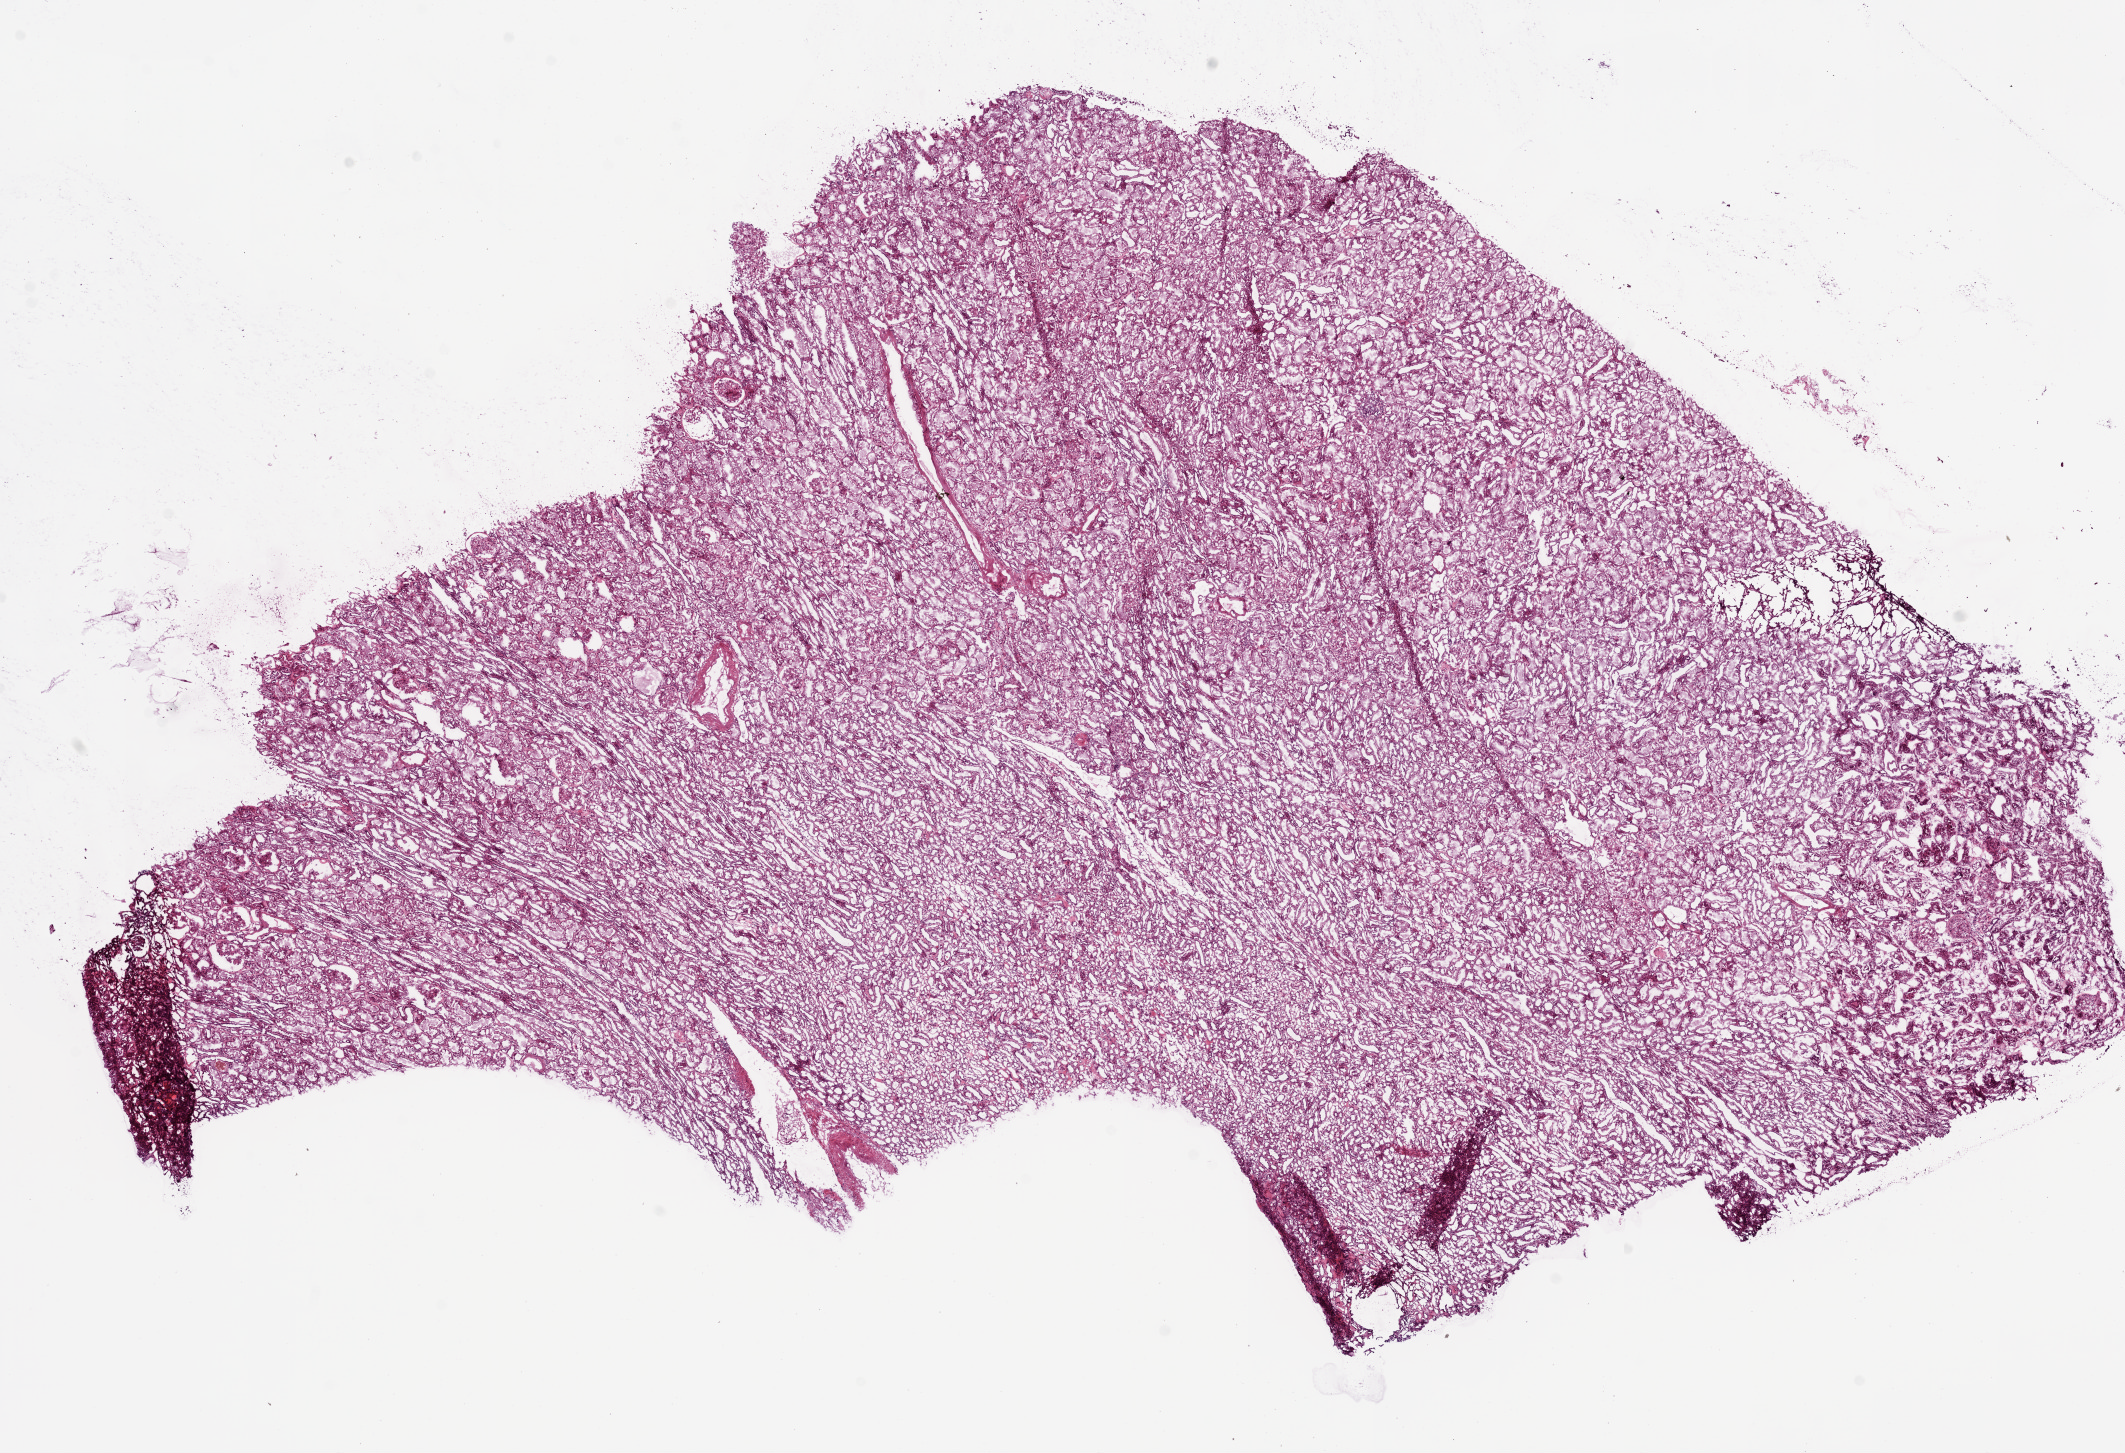
Whole-slide histology image, H&E-stained — low-resolution overview of the scanned area, about 17.1 x 11.7 mm (slide scanned at 20x), frozen section from the bottom of the tissue portion, solid tissue normal (non-tumour tissue) sample from the kidney. Female, age 68 years at initial diagnosis.
This section: solid tissue normal sample (biorepository sample class). Patient diagnosis: Clear cell adenocarcinoma, NOS.